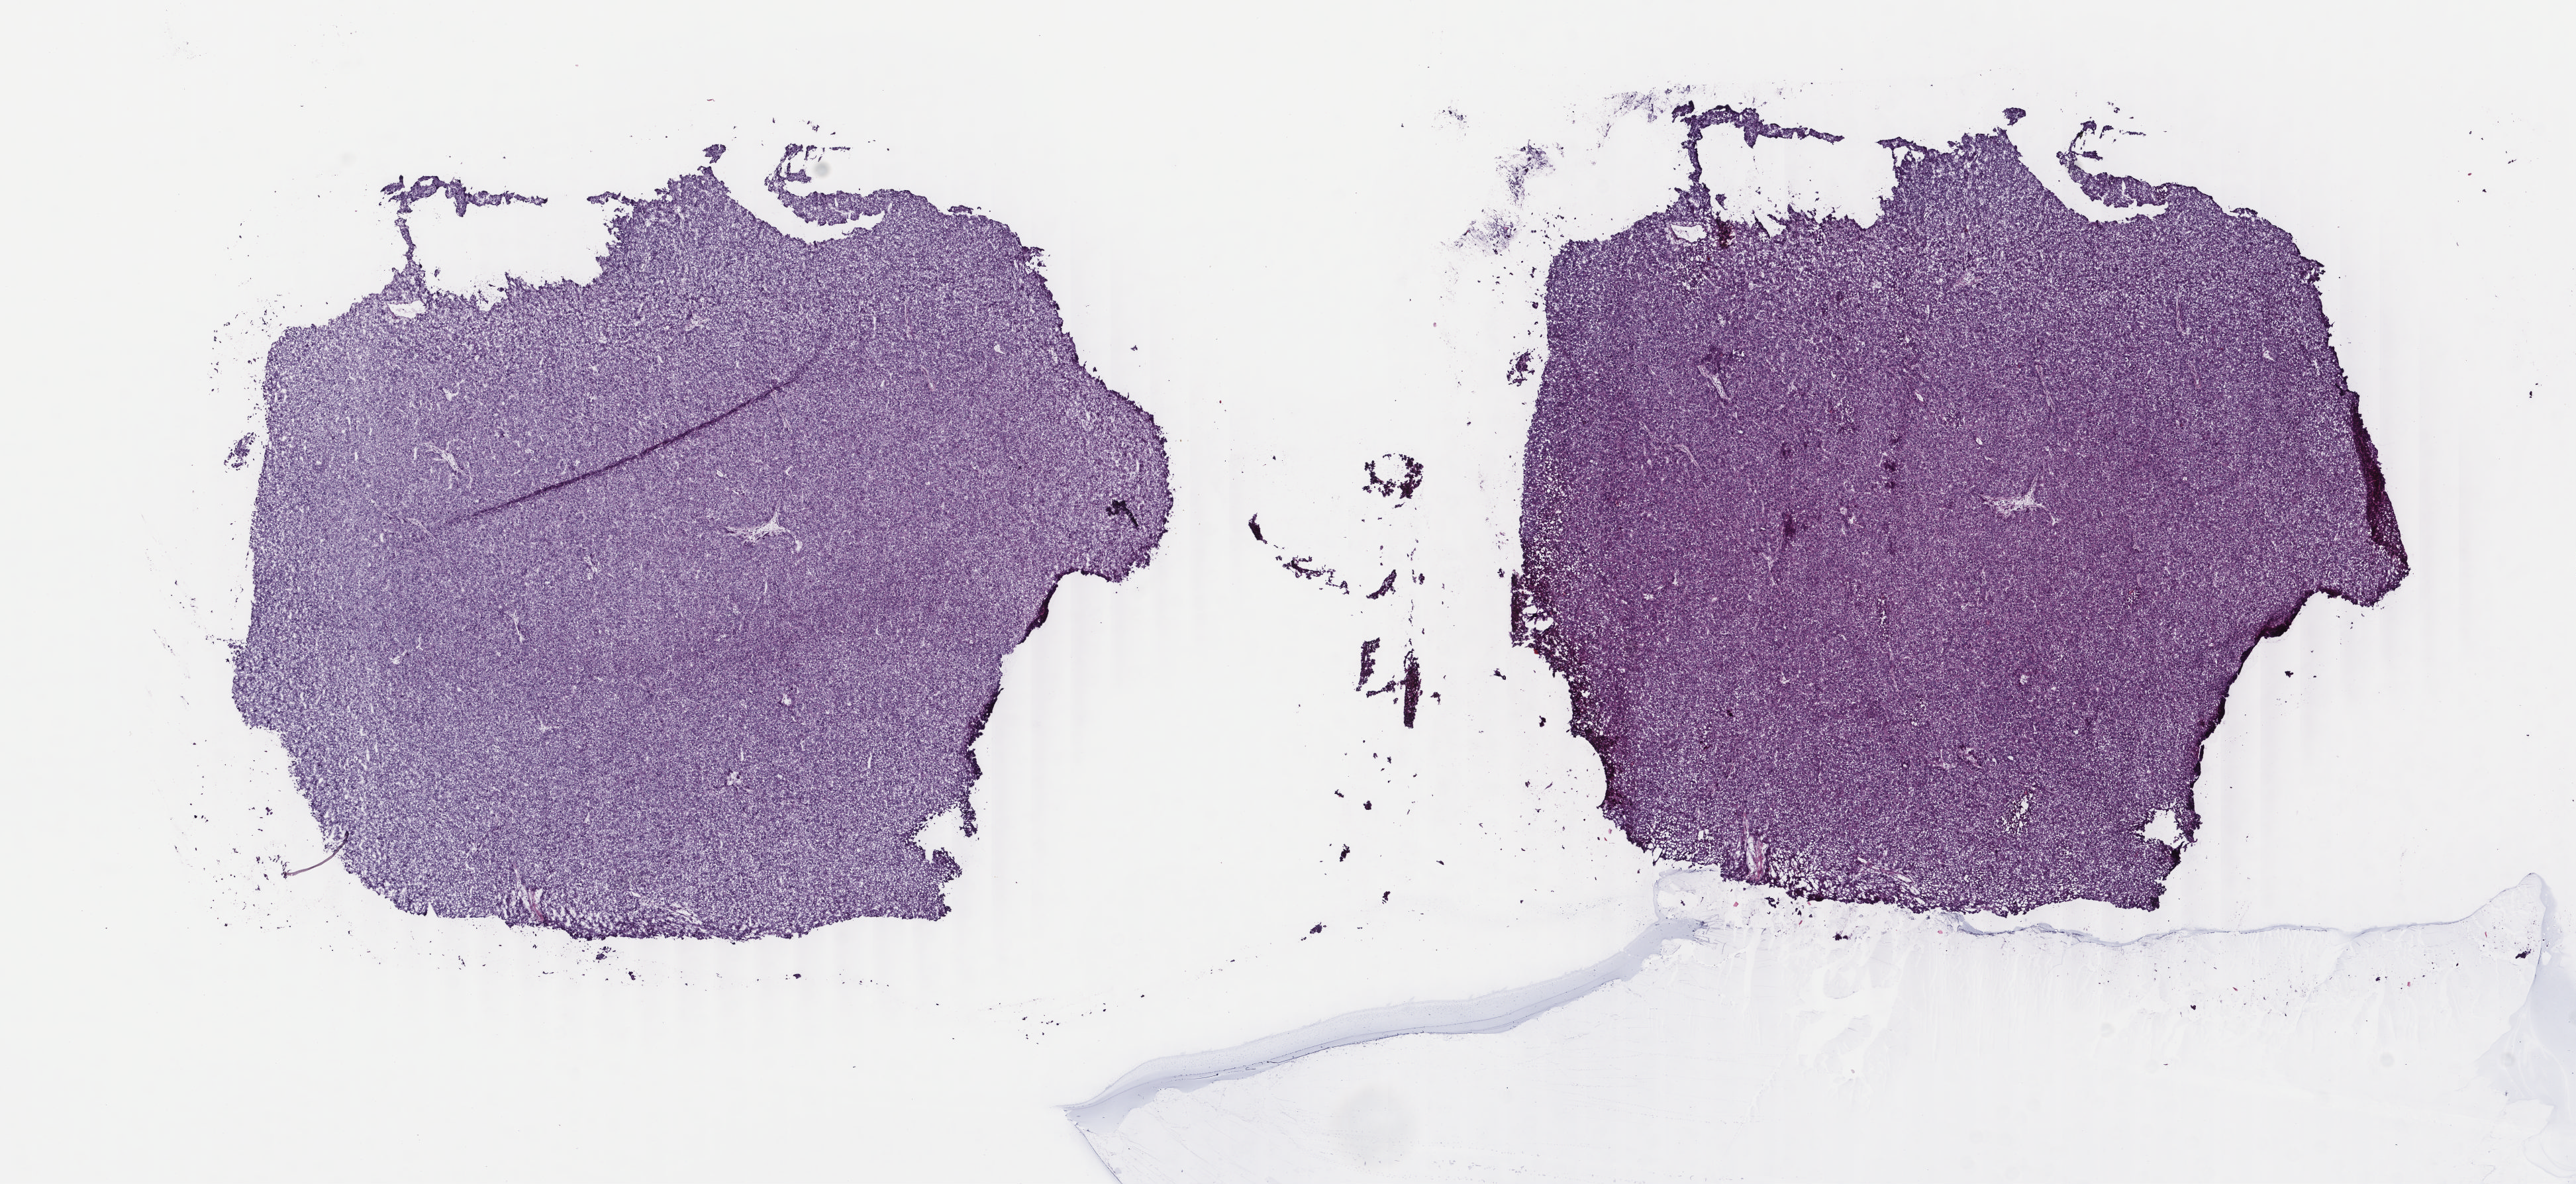
Whole-slide histology image, H&E, whole scanned area (about 15.5 x 7.1 mm, acquisition: 40x scan) shown as a low-resolution overview, frozen section from the bottom of the tissue portion, liver, primary tumour sample. Patient: male, age at initial diagnosis 73 years. Histologic grade: G2 (moderately differentiated). Slide review estimates, as recorded: tumour cells 90%, tumour nuclei 90%, normal cells 0%, stromal cells 10%, necrosis 0%. Inflammatory infiltration, as recorded: lymphocyte infiltration 2%, monocyte infiltration 0%, neutrophil infiltration 0%.
- diagnosis: Hepatocellular carcinoma, NOS
- AJCC pathologic stage: I (6th edition)